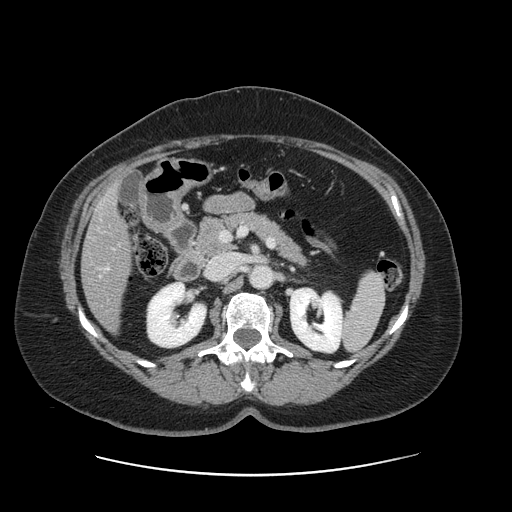
Contrast-enhanced abdominal CT, one axial slice. Slice 64 of 161 in the series (ordered by position). 120 kVp. Intravenous contrast given. Soft-tissue window (W 400 / L 40 HU). 2.5 mm slice thickness. 512 × 512 image matrix, field of view 398 × 398 mm. Female patient, age 62 years. From the clinical record (not read from this slice): diagnosis: colorectal cancer liver metastases, imaged before liver resection; multiple liver metastases: no; largest metastasis: 2.5 cm.
Outlined on this slice (expert manual segmentation):
- liver: bounding box (x1, y1, x2, y2) in pixels: (82, 188, 131, 329)